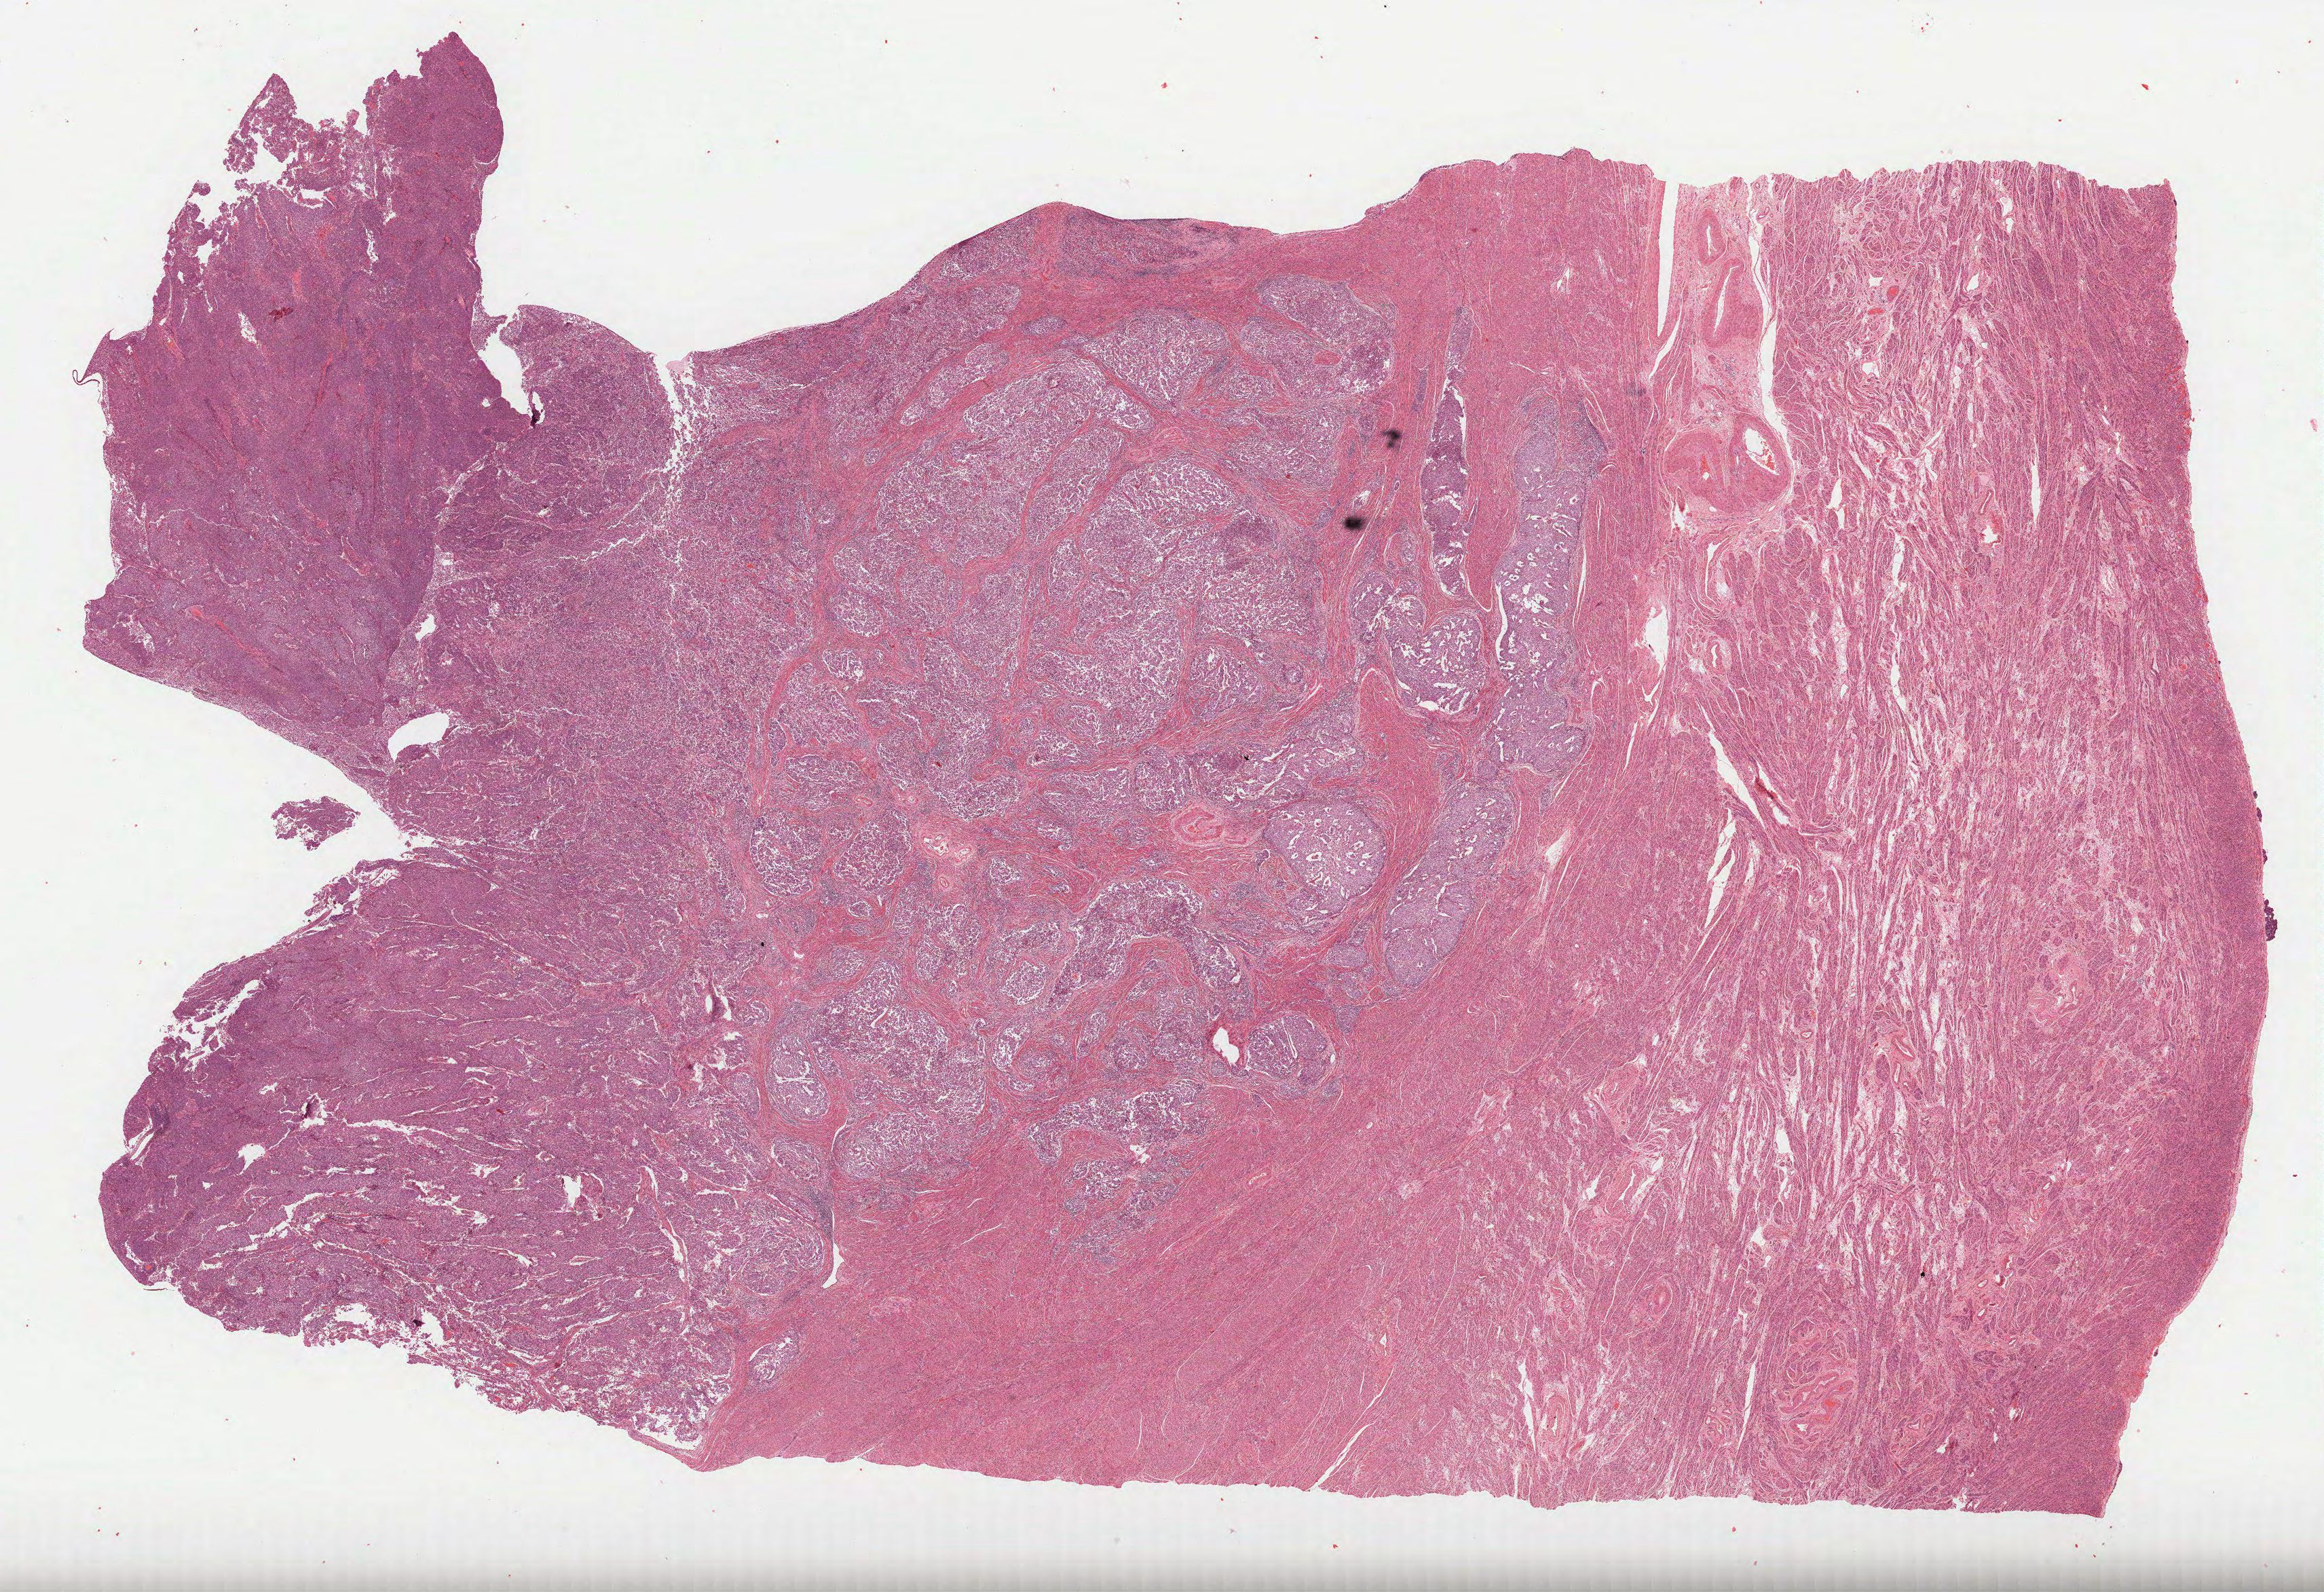
Hematoxylin and eosin (H&E) stained whole-slide image — a low-resolution overview of the entire scanned area, about 27.6 x 18.9 mm (from a 40x scan). FFPE section. Sample: primary tumour, uterus. Female patient; age at initial diagnosis 65 years. Histologic grade: G3 (poorly differentiated).
• FIGO stage: IB
• diagnosis: Endometrioid adenocarcinoma, NOS (endometrium)